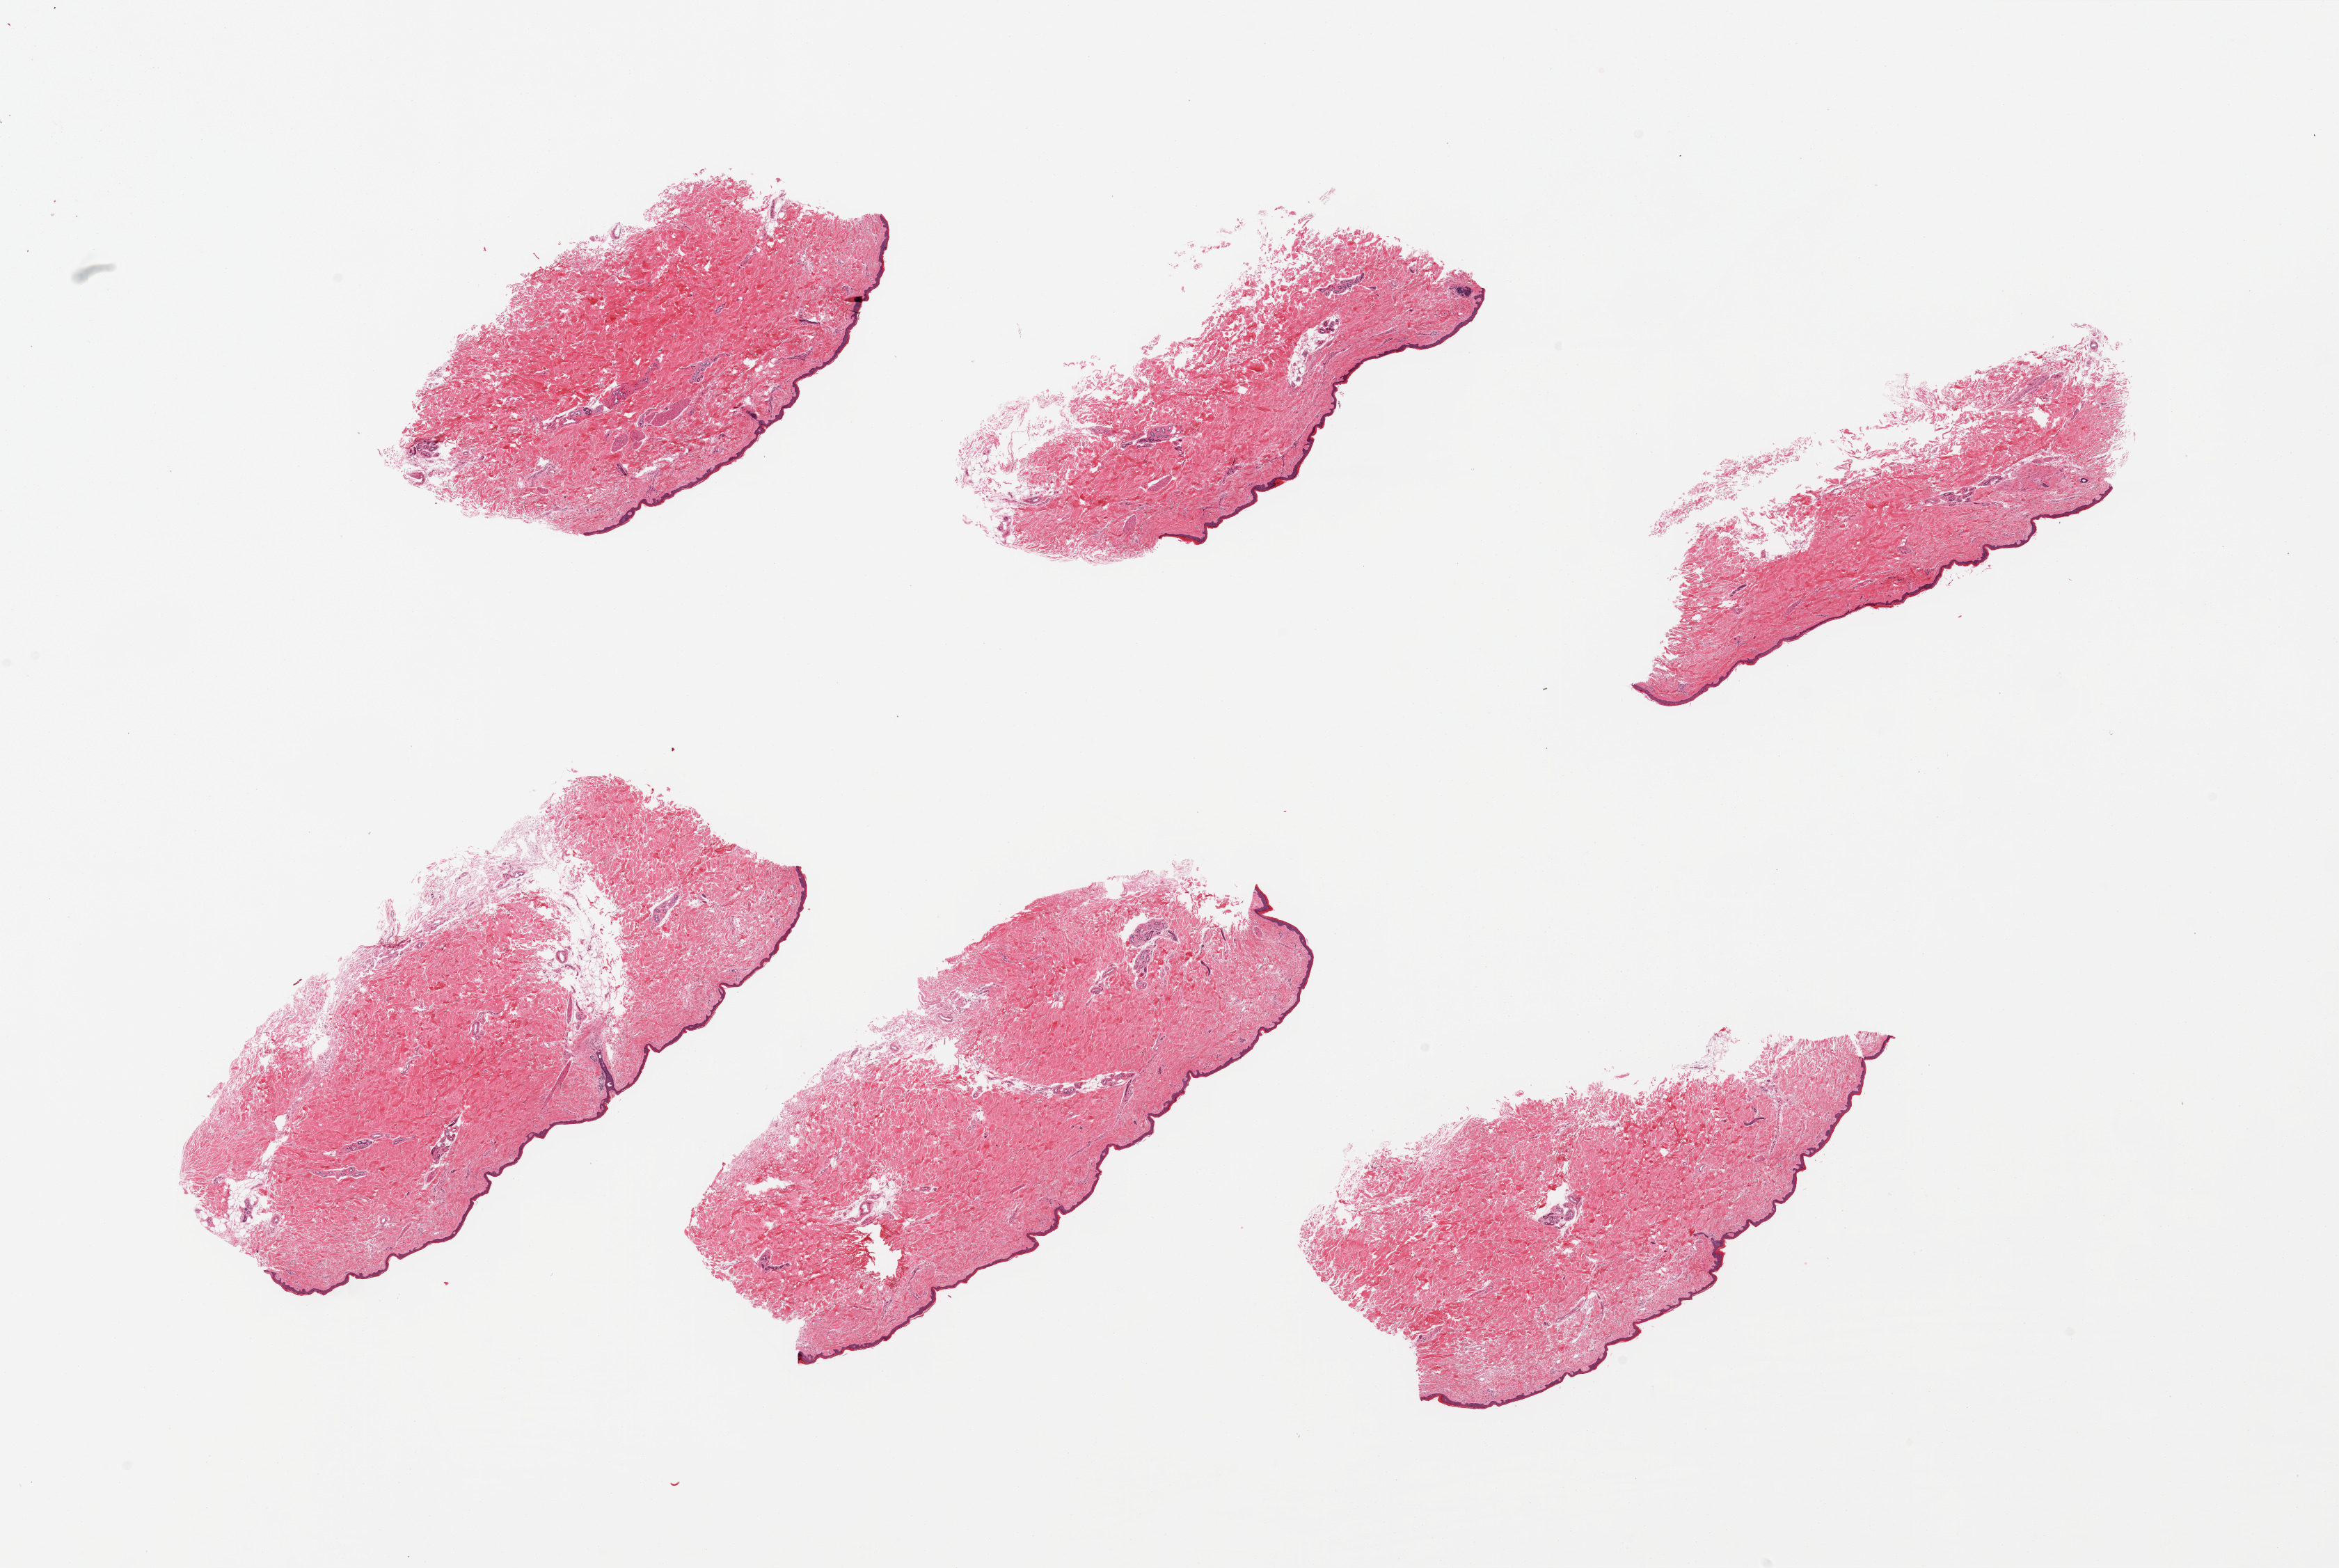
Hematoxylin and eosin (H&E) whole-slide image, brightfield, a low-resolution overview of the entire scanned area, about 26.6 x 17.8 mm, PAXgene-fixed, paraffin-embedded tissue, target tissue: skin of lower leg, donor tissue sample. Male donor.
Review note (as recorded): 6 pieces, squamous epithelium is ~50 microns.